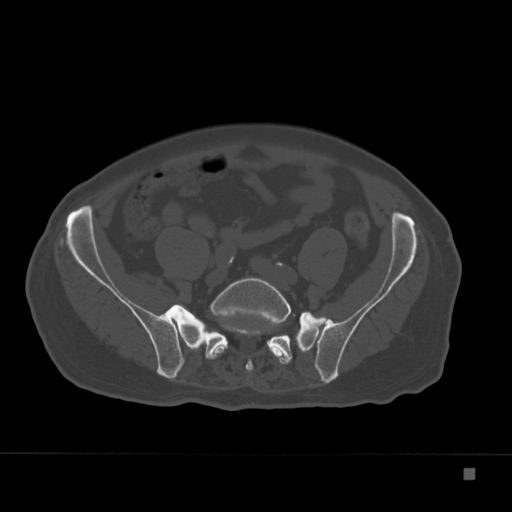
CT including the spine, one axial slice. Slice 14 of 332 in the series (ordered by position). Bone window (W 1800 / L 400 HU). 1.5 mm slice thickness. 512 × 512 image matrix. Male patient, age 72 years. From the clinical record (not read from this slice): primary cancer: skeletal.
Annotated regions visible in this slice (semi-automatically segmented with operator editing):
- L5 vertebra: bounding box <206,278,292,372> (left, top, right, bottom; pixels)